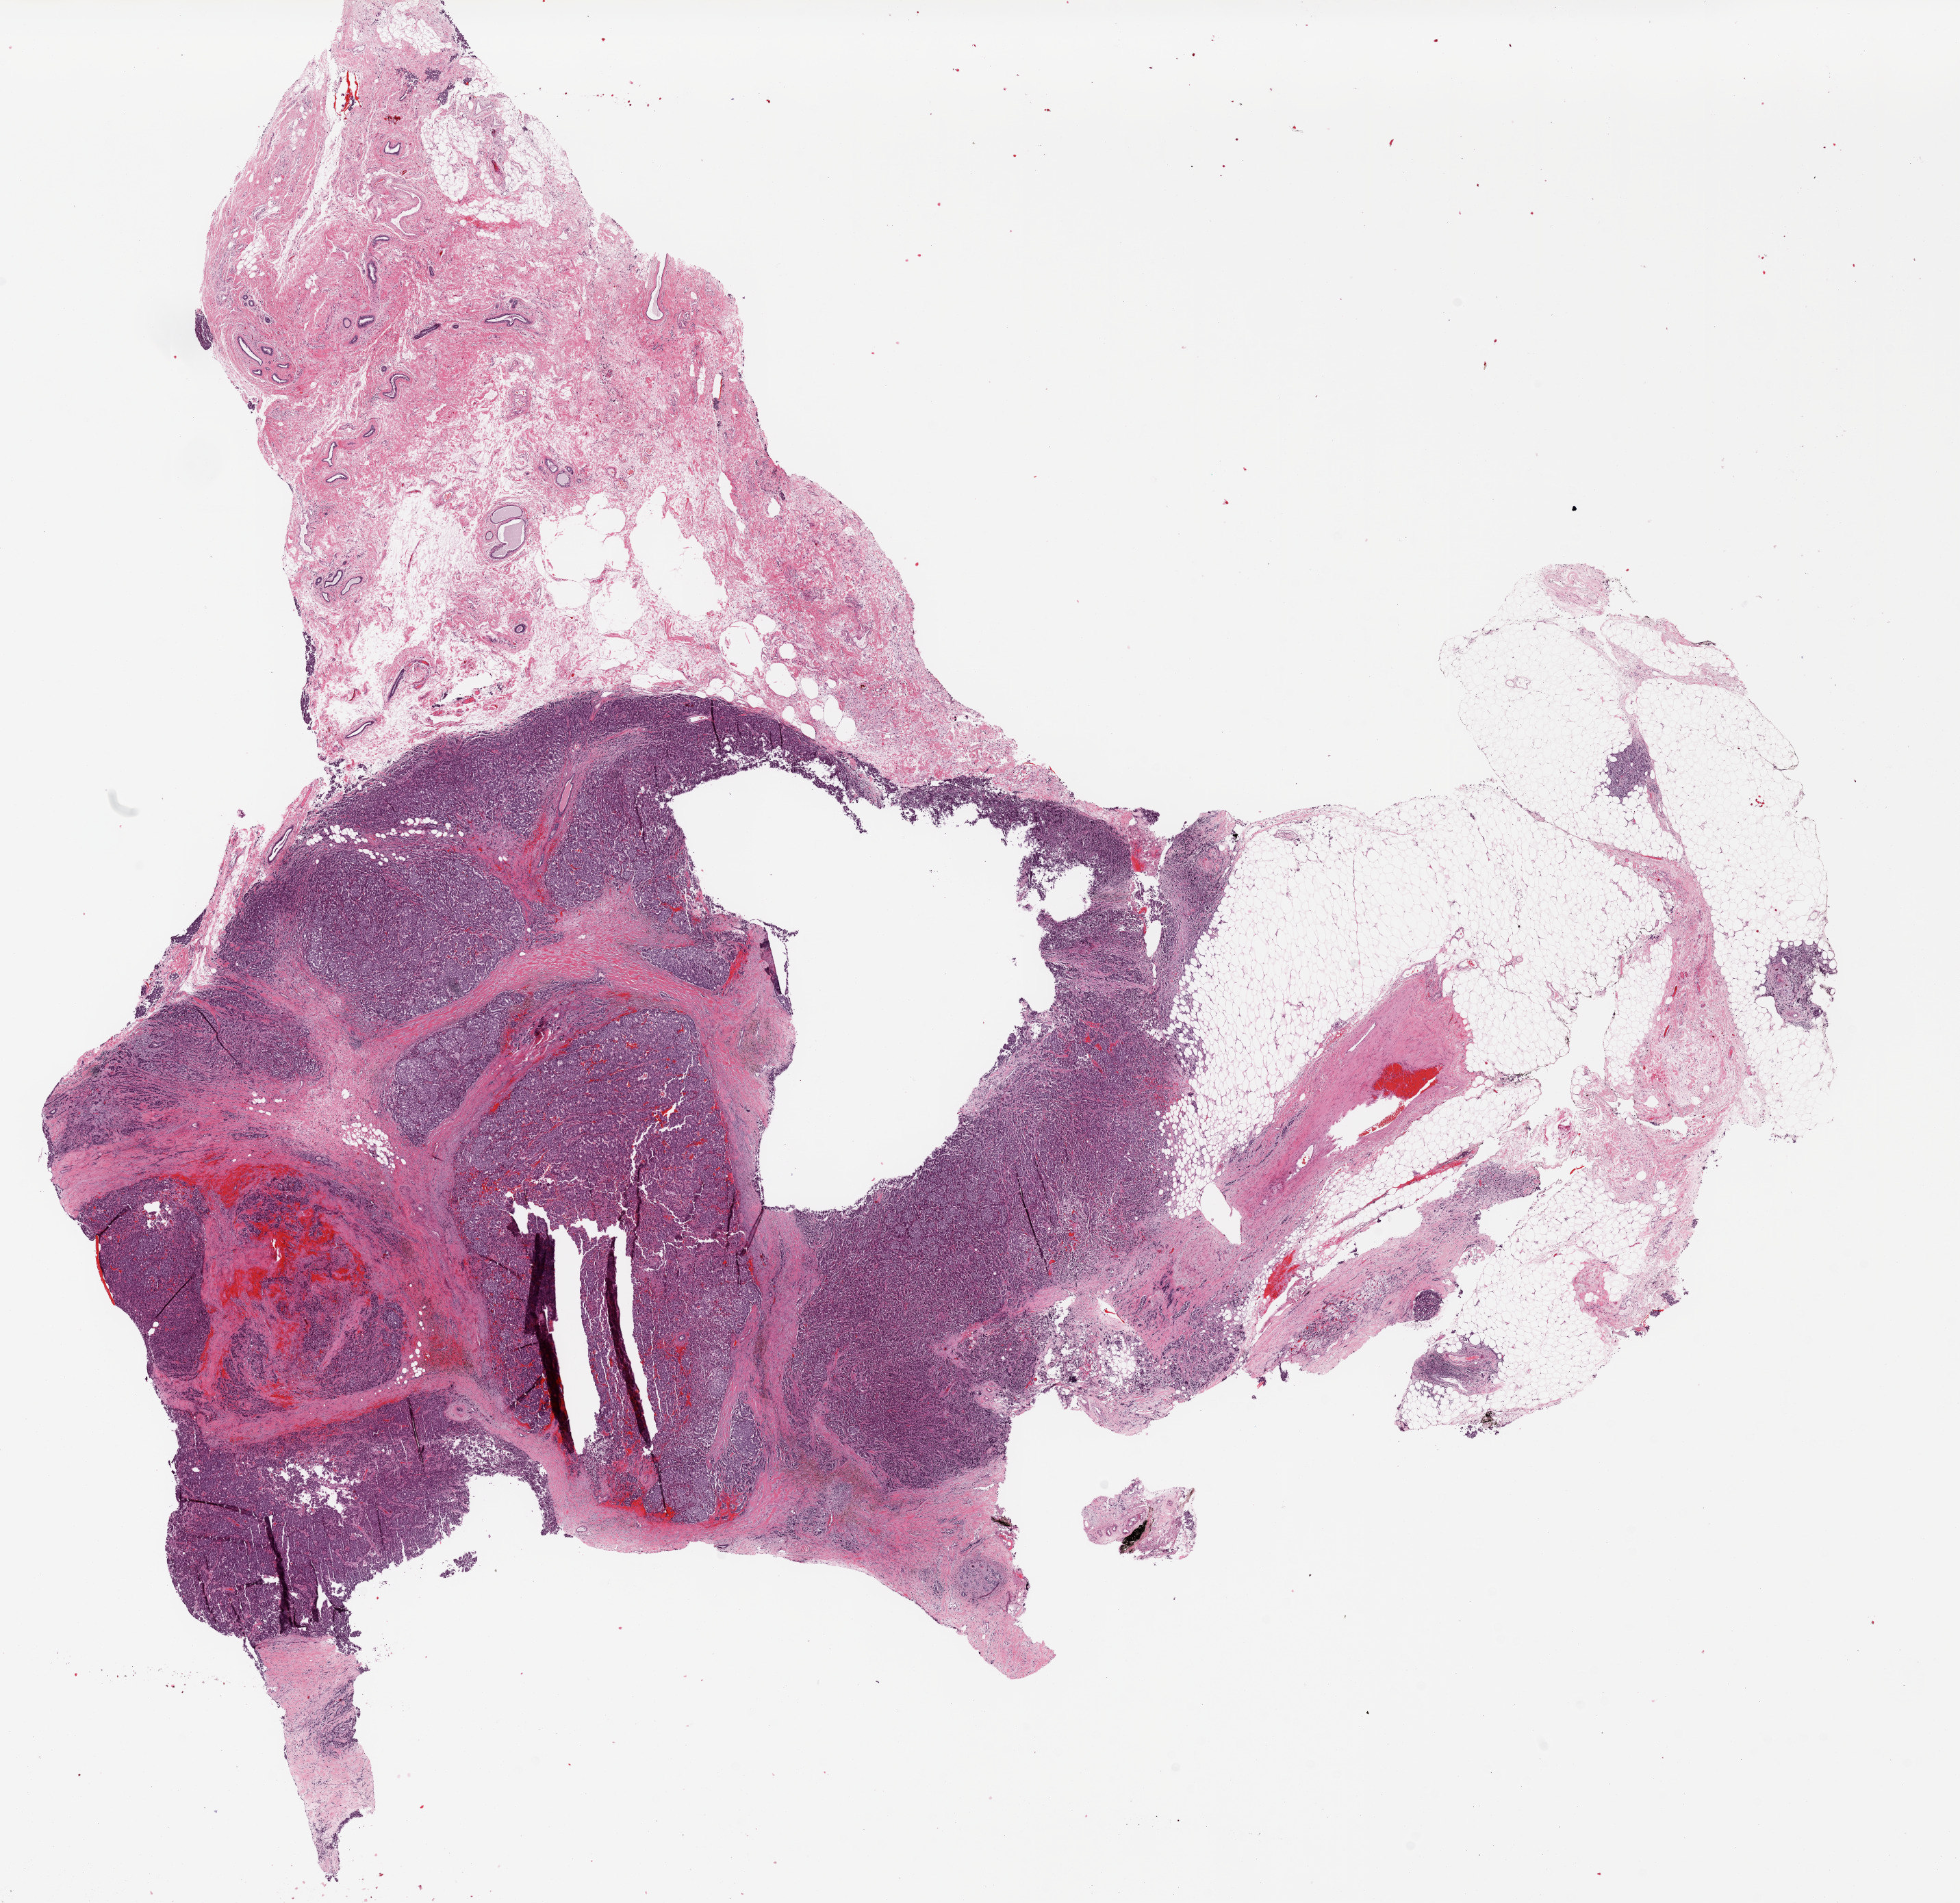
H&E-stained whole-slide image — shown as a low-resolution overview of the whole scanned area (about 22.9 x 22.2 mm, slide scanned at 20x), formalin-fixed paraffin-embedded (FFPE) diagnostic section, primary tumour sample from the breast. Female, age 67 years at initial diagnosis.
Diagnosis: Infiltrating duct mixed with other types of carcinoma. AJCC pathologic stage: IIB.